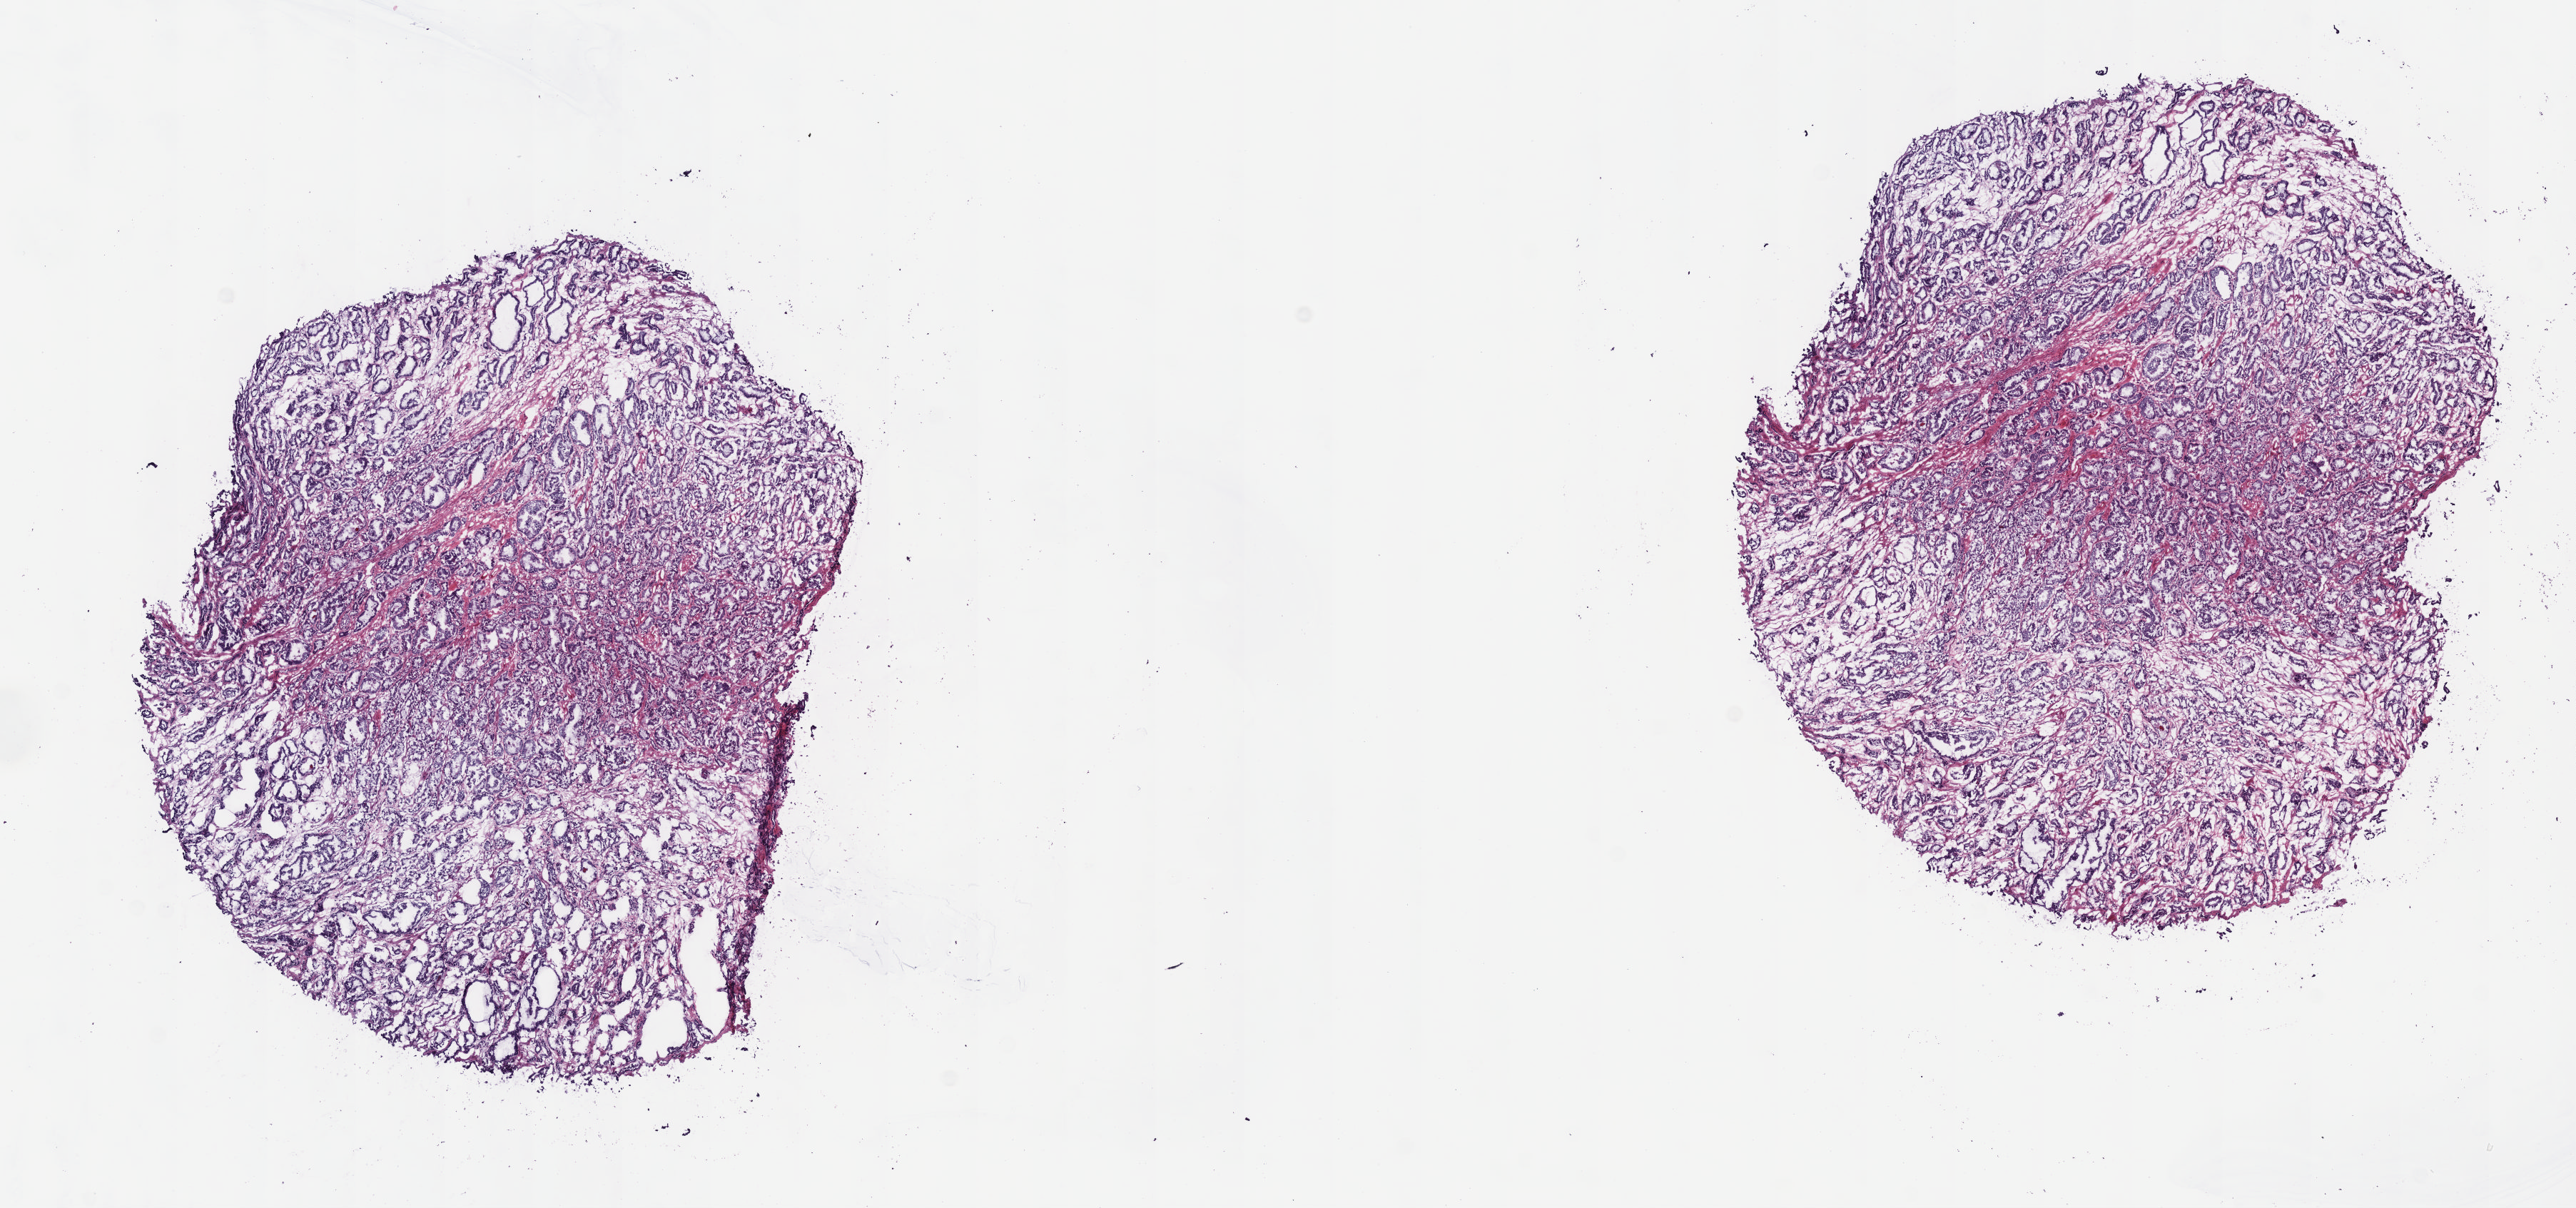
H&E-stained whole-slide image, shown as a low-resolution overview of the whole scanned area (about 14.6 x 6.8 mm), frozen section, primary tumour sample from the prostate. Male, age 53 years at initial diagnosis. Gleason score: 6 (3+3). Slide review estimates, as recorded: tumour cells 85%, tumour nuclei 90%, normal cells 0%, stromal cells 15%, necrosis 0%. Inflammatory infiltration, as recorded: lymphocyte infiltration 0%, monocyte infiltration 0%, neutrophil infiltration 0%.
Diagnosis: Adenocarcinoma, NOS (prostate gland).